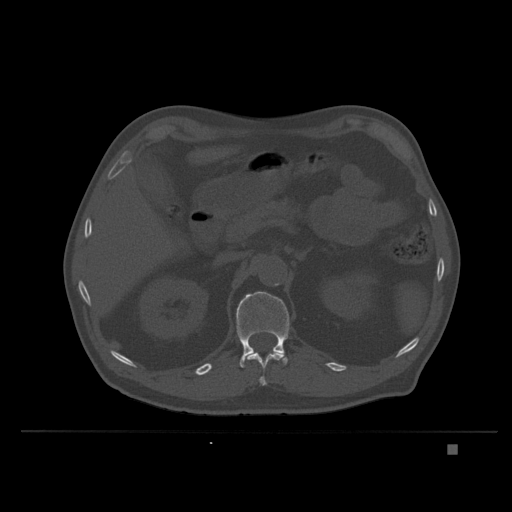
CT including the spine, one axial slice; position 146 of 435 along the scan axis; bone window (W 1800 / L 400 HU); 1.5 mm slice thickness; 512 × 512 image matrix. Patient: male, 73 years. Case-level facts recorded for this patient, not image findings: primary cancer: skin.
Outlined on this slice (semi-automatically segmented with operator editing):
- L1 vertebra: bounding box [x1, y1, x2, y2] px = [236, 291, 290, 368]
- T12 vertebra: [245, 350, 285, 386]